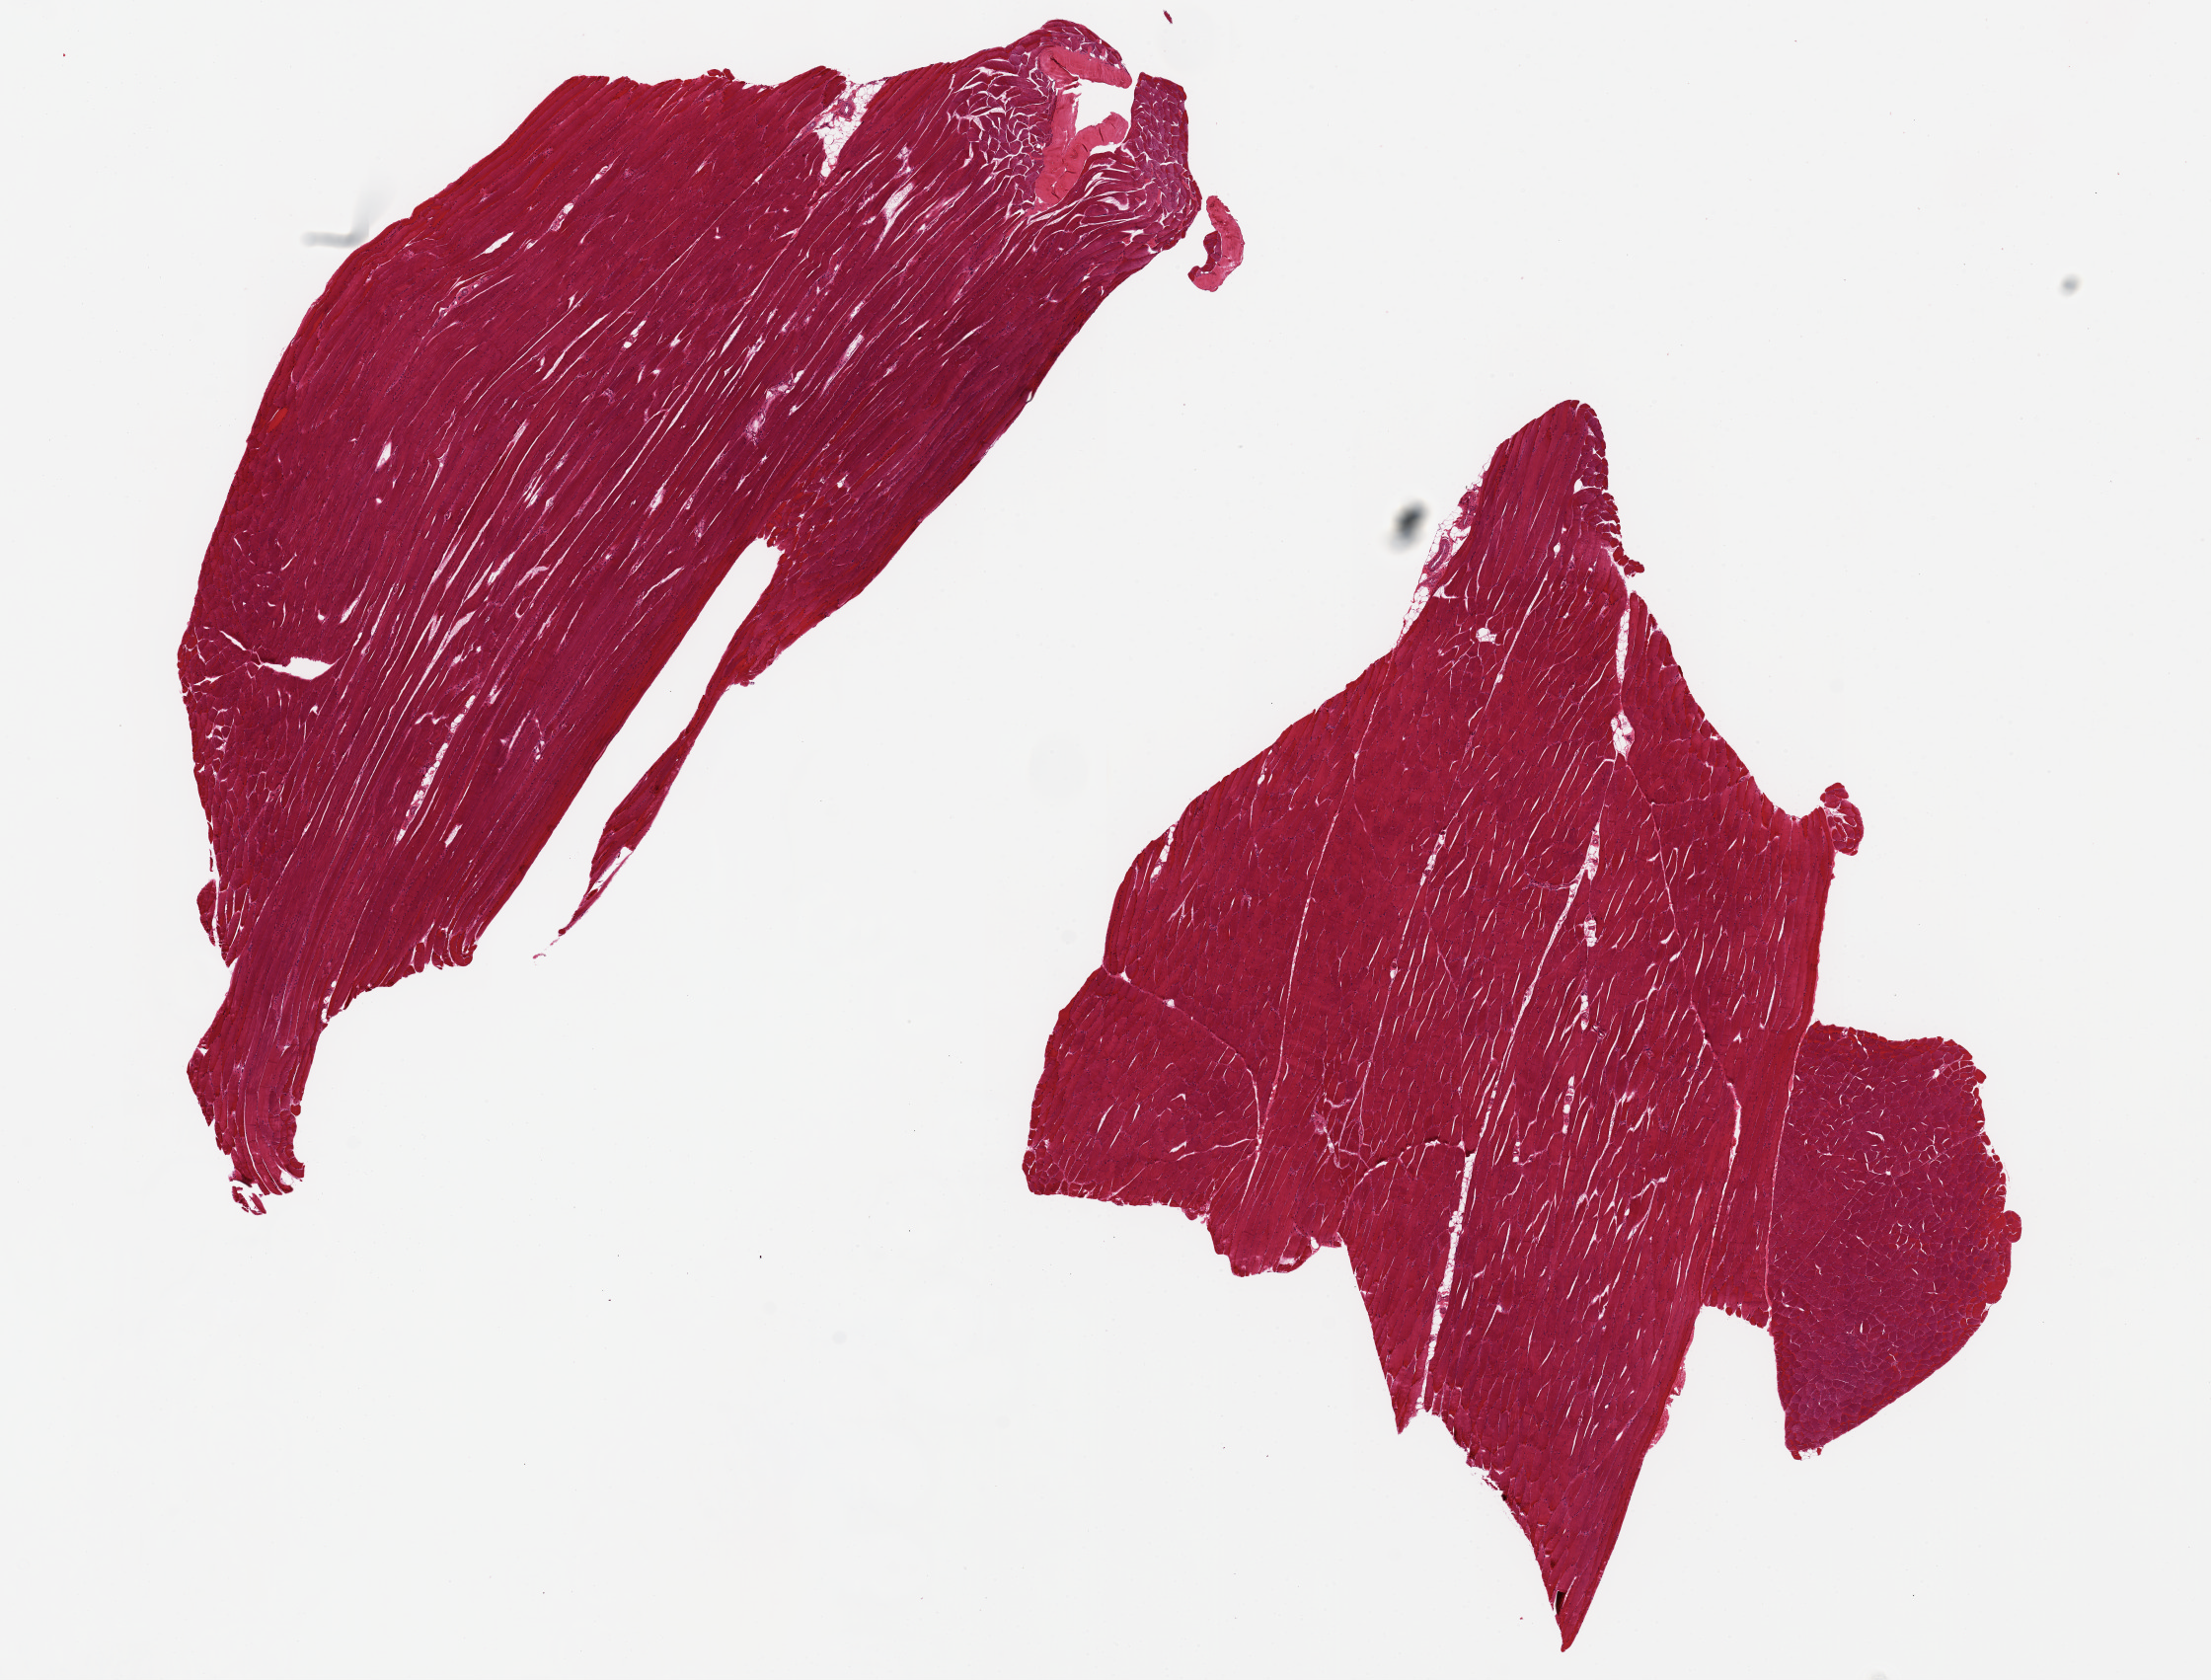
H&E whole-slide image, brightfield, shown as a low-resolution overview of the whole scanned area (about 17.7 x 13.5 mm, slide scanned at 20x); PAXgene-fixed, paraffin-embedded tissue; section of skeletal muscle (target tissue); donor tissue sample. Donor: male.
Review note (as recorded): 2 pieces~11x5mm,10x7mm.